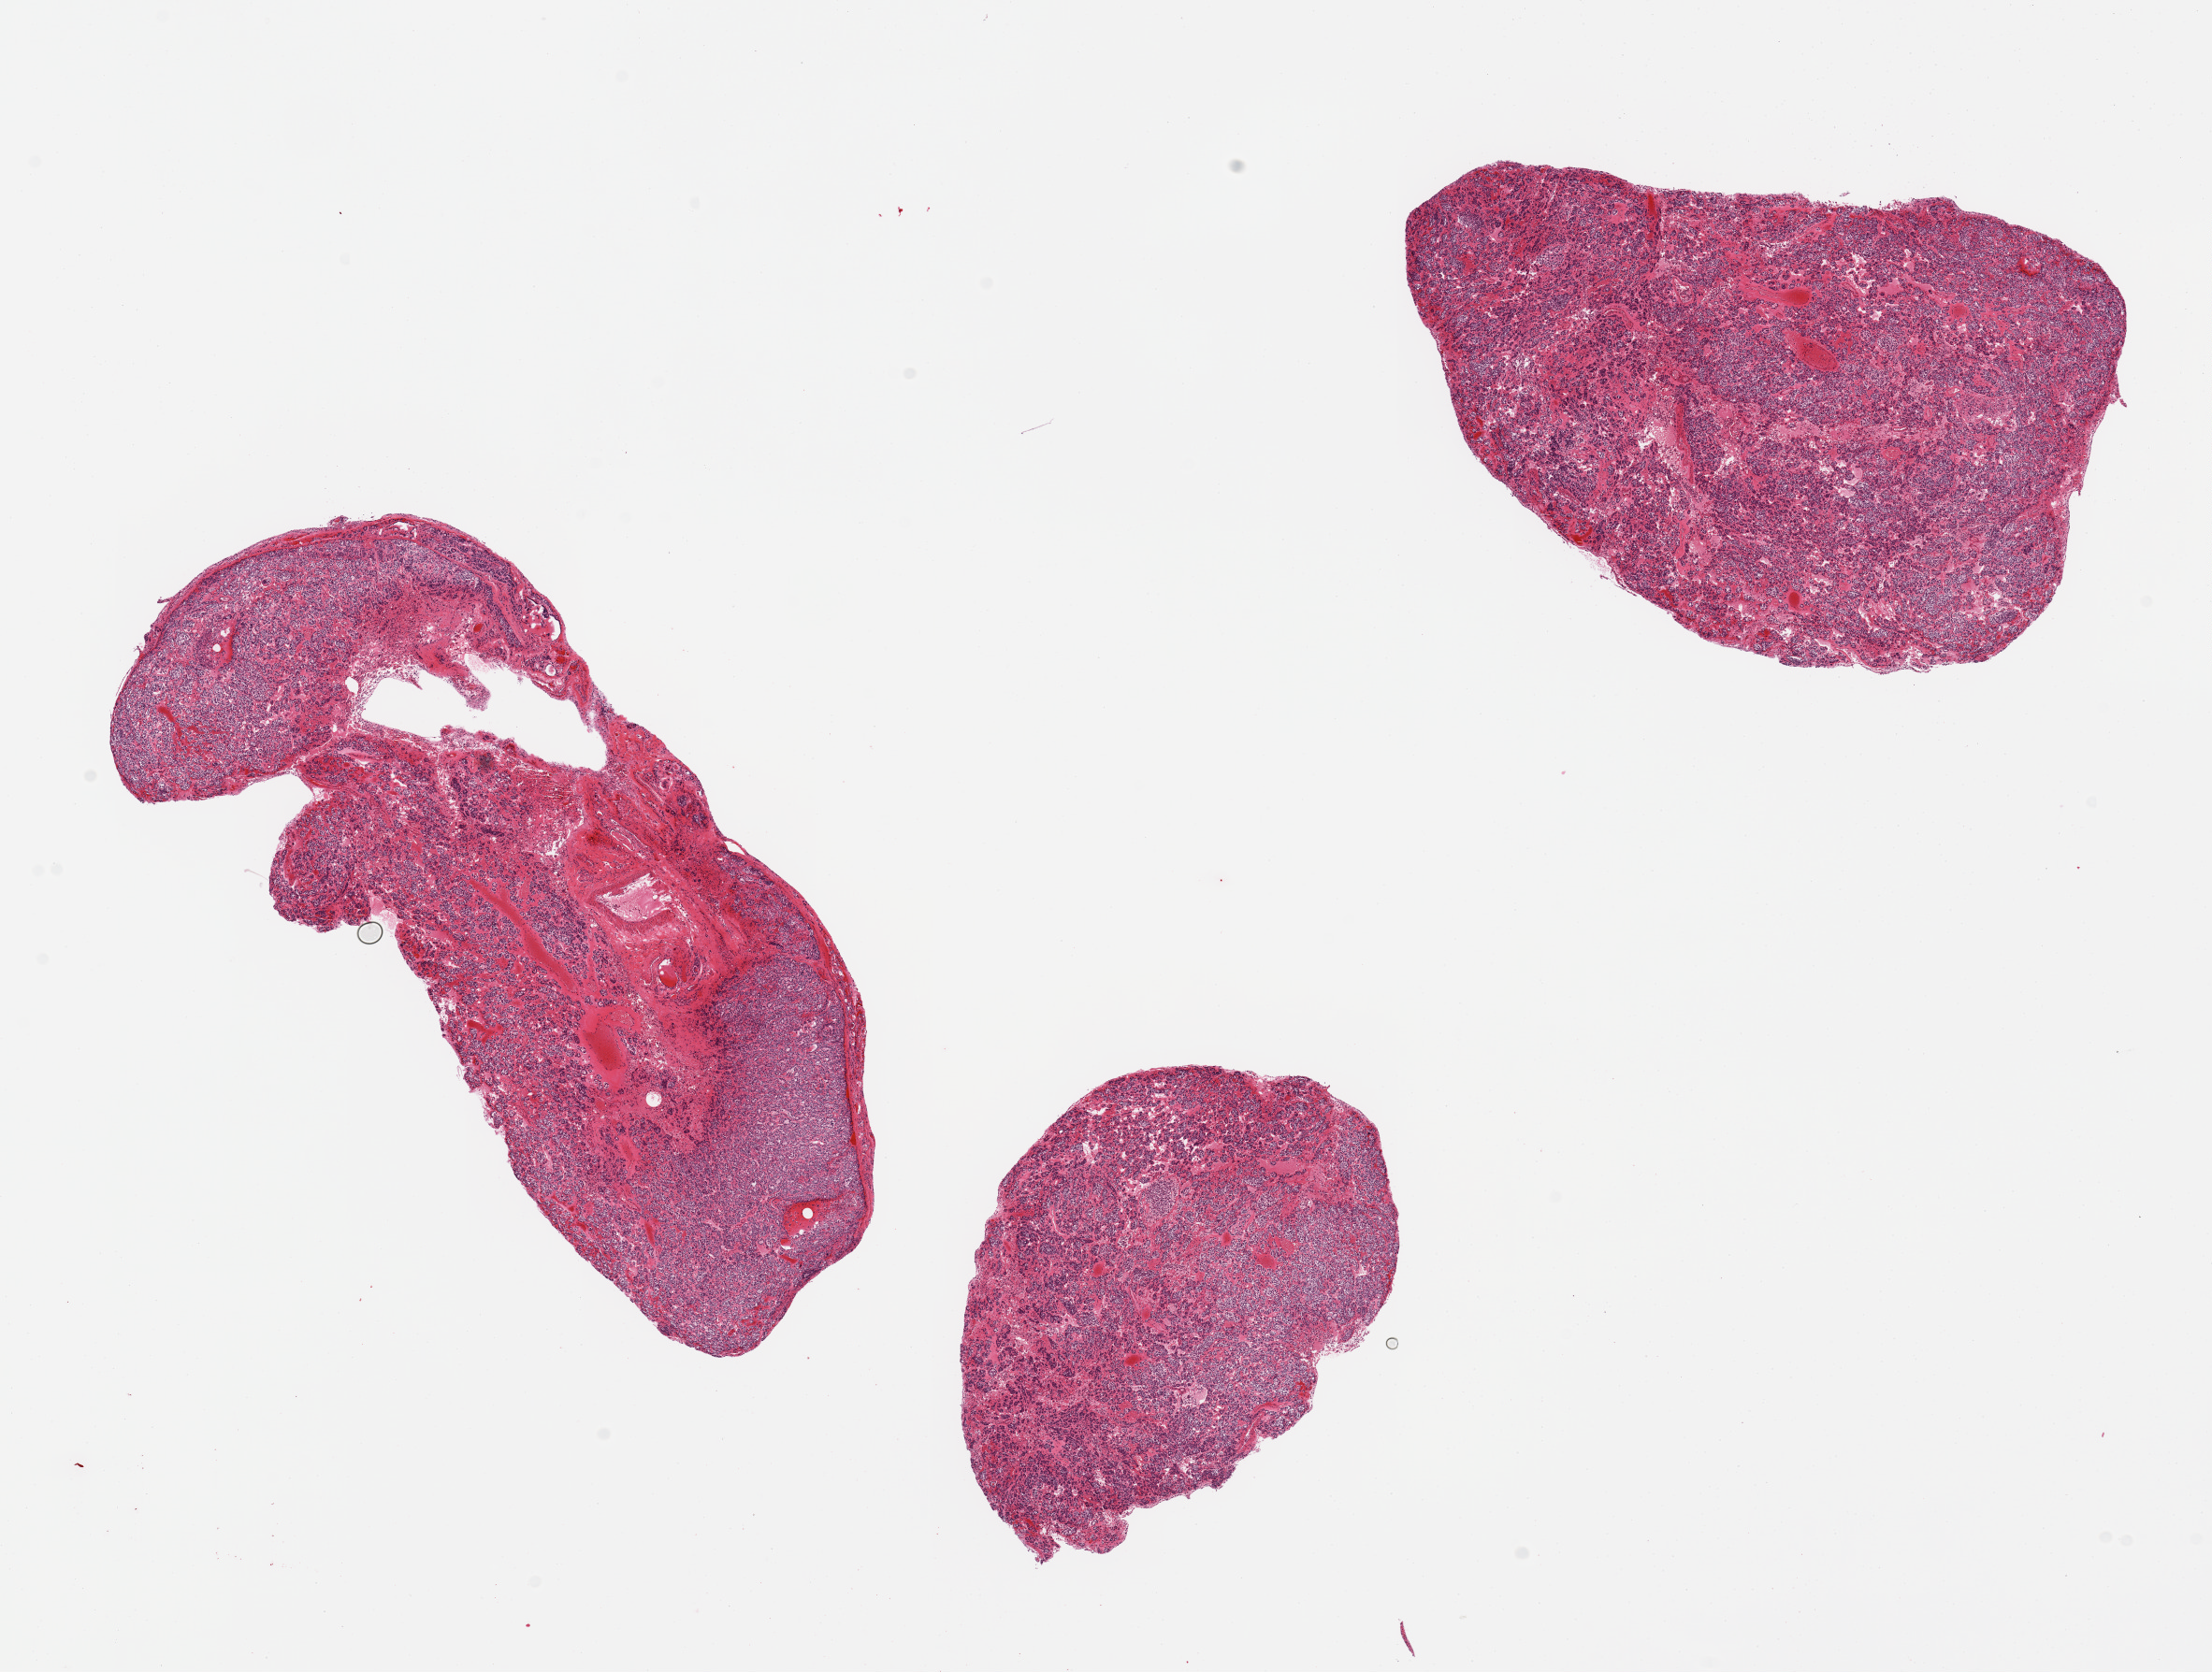
Hematoxylin and eosin (H&E) whole-slide image, brightfield — a low-resolution overview of the entire scanned area, about 18.7 x 14.1 mm (from a 20x scan); PAXgene-fixed, paraffin-embedded tissue; section of thyroid (target tissue); donor tissue sample. Donor sex: male.
* review note (as recorded): 3 pieces, favor medullary carcinoma, involving the entire specimen (up to 8mm in greatest dimension)